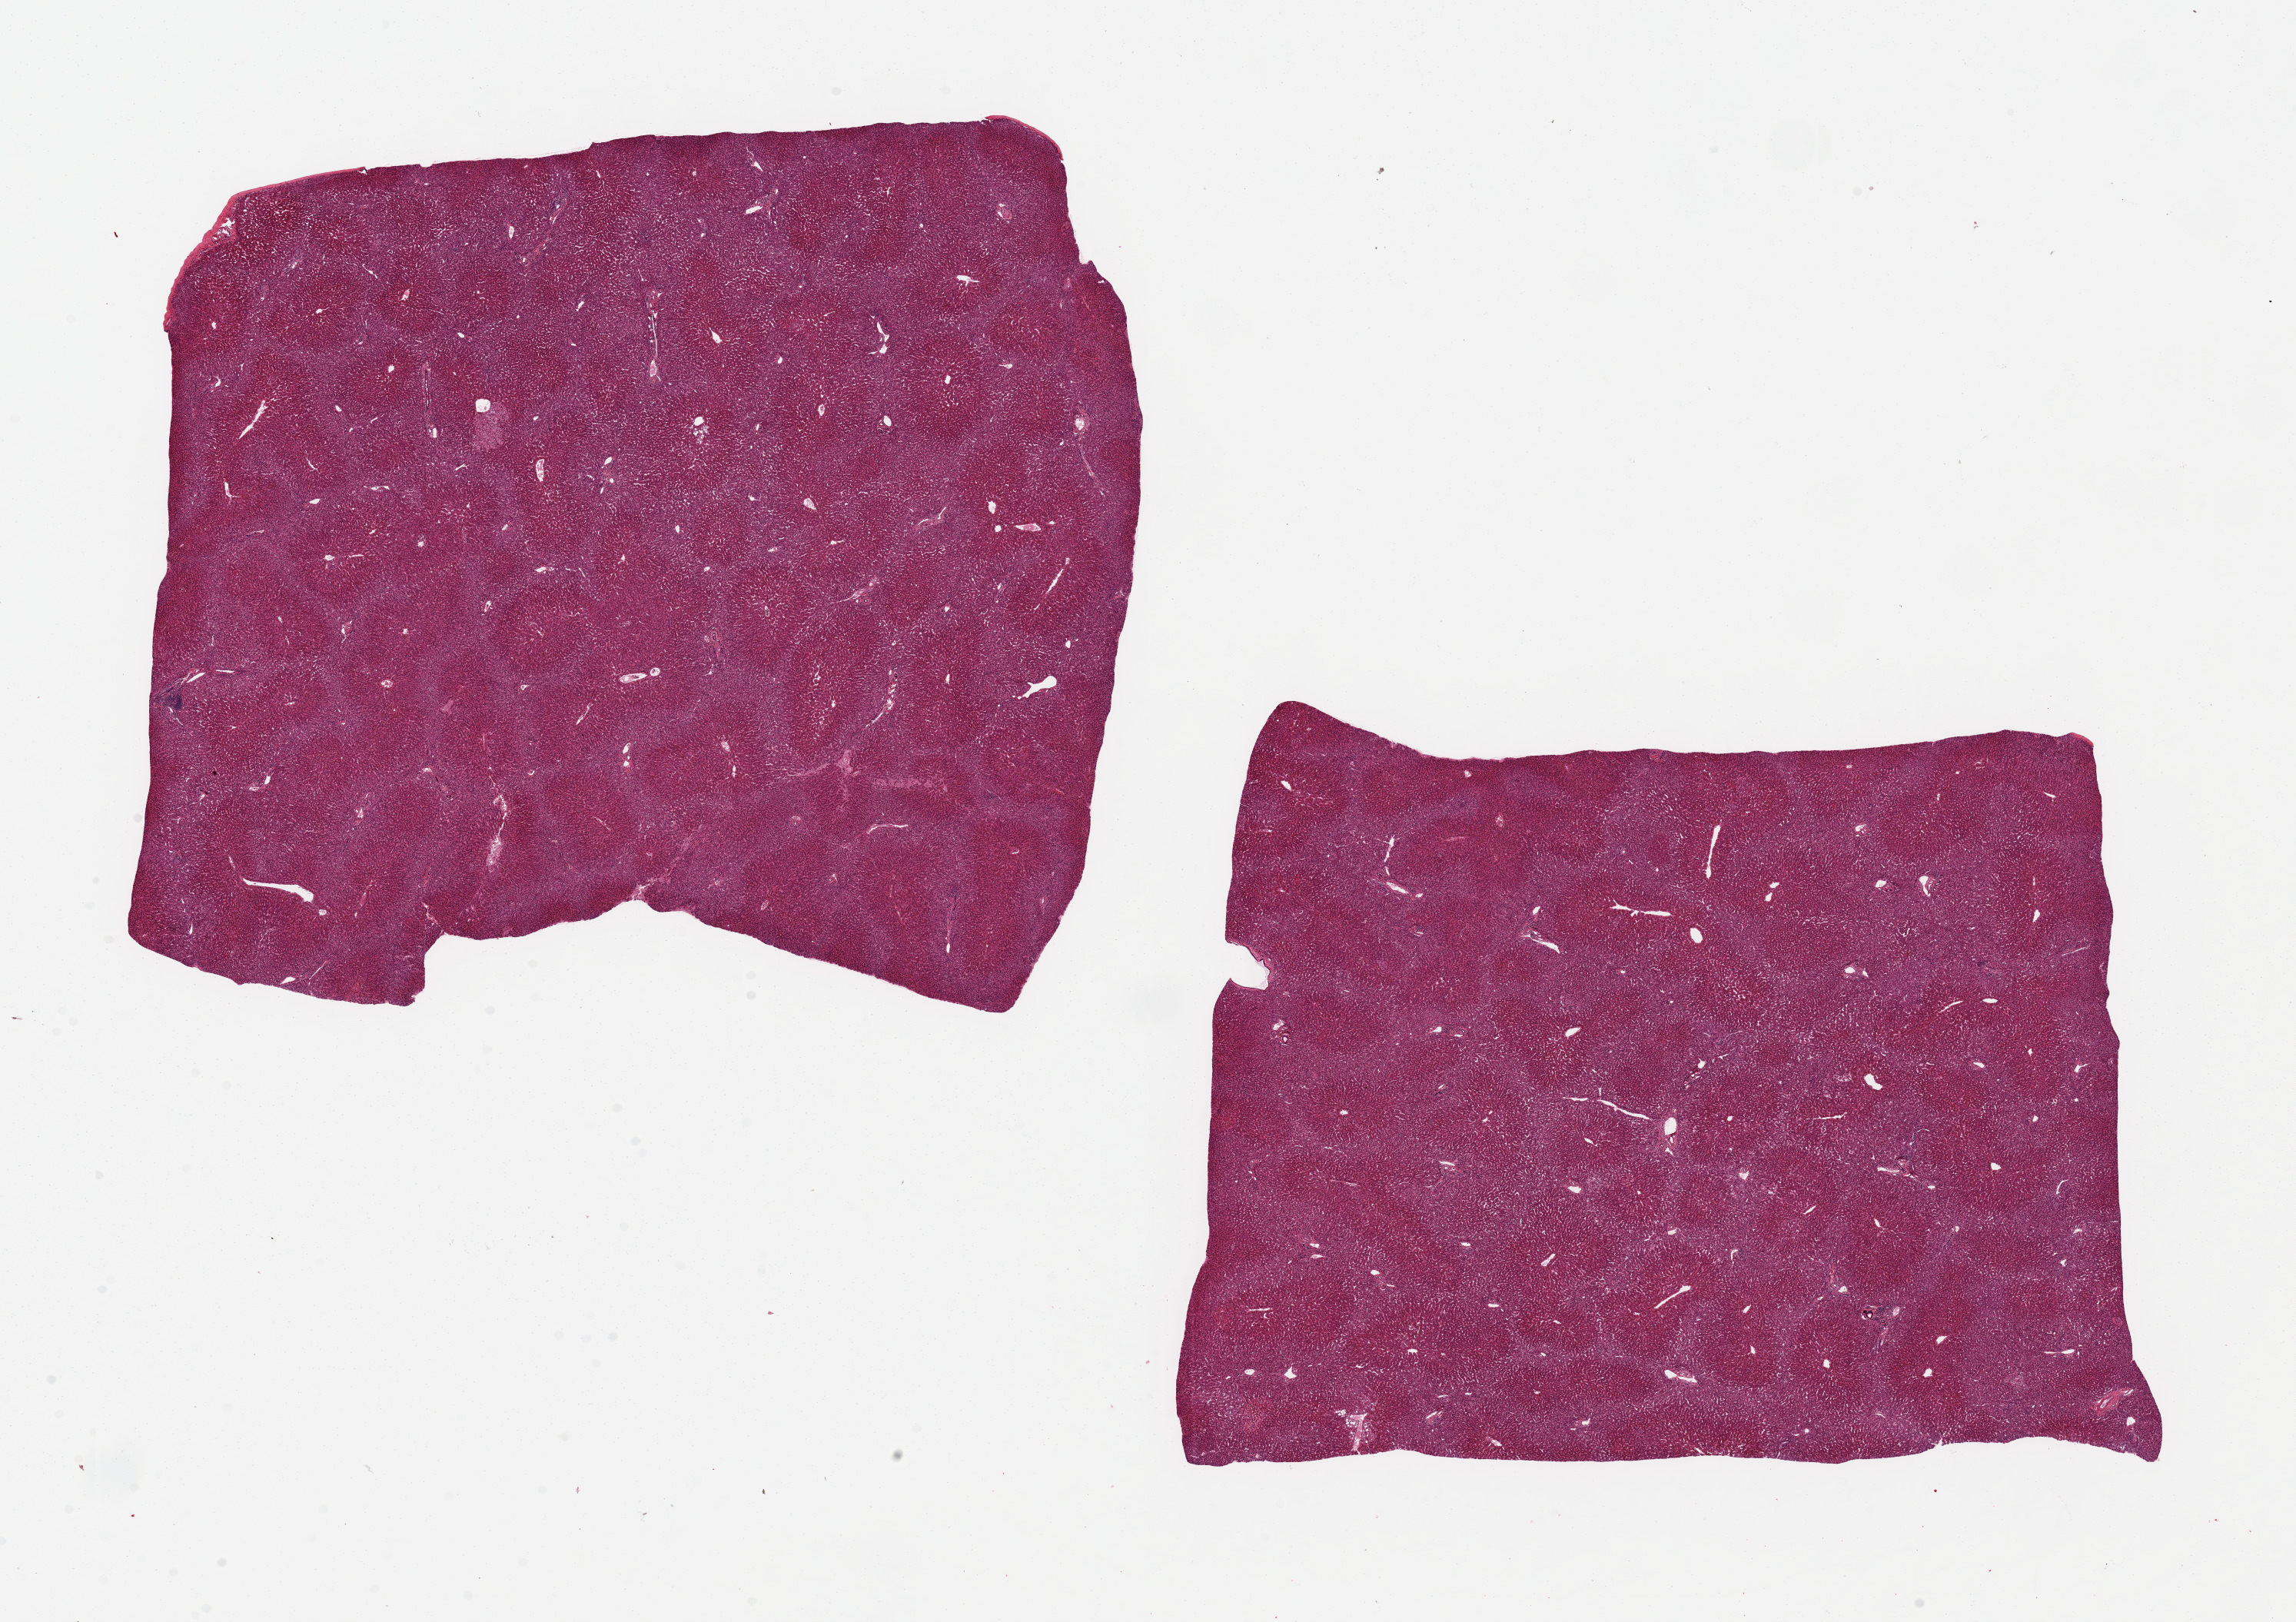
Whole-slide image, haematoxylin and eosin stain — low-resolution overview of the scanned area, about 23.6 x 16.7 mm (slide scanned at 20x), PAXgene-fixed paraffin-embedded (PFPE) section, target tissue: liver, donor tissue sample. Donor: female.
* reviewer comment on this tissue sample: 2 ~9X8mm aliquots, extensive patterned microvesicular steatosis ? drug/toxic effect